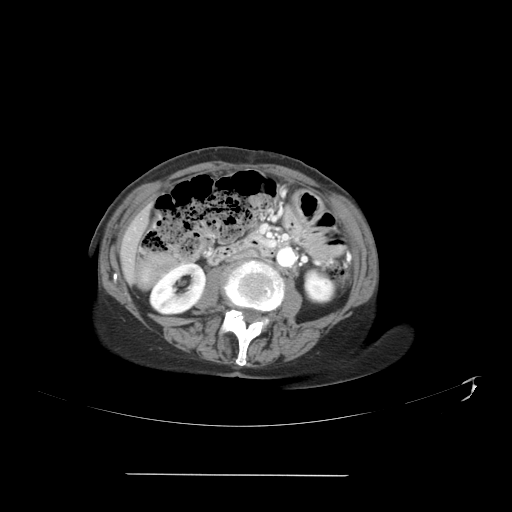
Contrast-enhanced abdominal CT, one axial slice; intravenous contrast given; soft-tissue window (W 400 / L 40 HU); 5 mm slice thickness; 512 × 512 image matrix. Female patient, age 74 years. From the clinical record (not read from this slice): diagnosis: colorectal cancer liver metastases, imaged before liver resection; multiple liver metastases: yes; largest metastasis: 3.3 cm; disease in both lobes: yes.
Structures marked on this image (expert manual segmentation):
- liver: bounding box <124,216,145,276> (left, top, right, bottom; pixels)
- planned liver remnant (the part of the liver to remain after resection): <127,216,145,243>